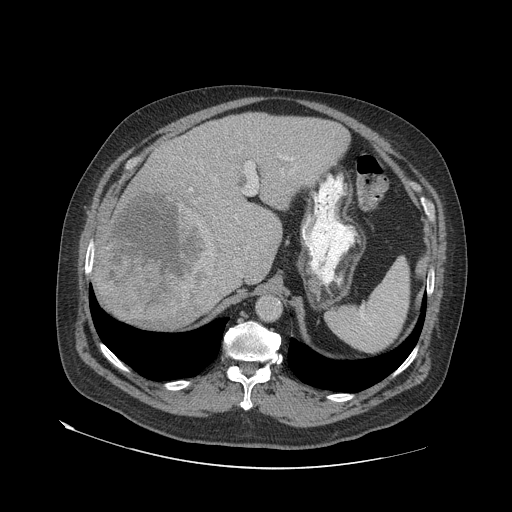
Contrast-enhanced abdominal CT (liver protocol), one axial slice; position 48 of 79 along the scan axis; reconstruction kernel STANDARD; 140 kVp; soft-tissue window (W 400 / L 40 HU); 512 × 512 image matrix, field of view 480 × 480 mm. From the clinical record (not read from this slice): diagnosis: hepatocellular carcinoma (patient treated with transarterial chemoembolisation; whether this scan precedes or follows treatment is not stated here); TNM stage (as recorded): Stage-IVA.
Annotated regions visible in this slice (semi-automatic segmentation, software-assisted and operator-edited):
- liver parenchyma outside the tumour (the mass and vessels are separate outlines, so this box may not span the whole liver): bounding box <94,112,350,324> (left, top, right, bottom; pixels)
- mass: <100,193,218,323>
- liver vessels: <190,155,294,222>